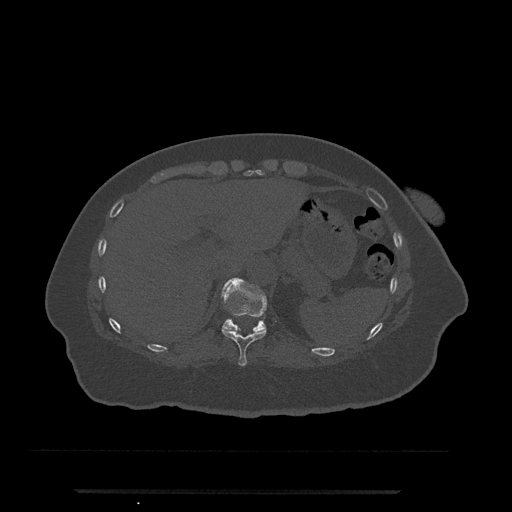
CT including the spine, one axial slice; position 262 of 797 along the scan axis; reconstruction kernel Br40s/3; 120 kVp; bone window (W 1800 / L 400 HU); 0.5 mm slice thickness; 512 × 512 image matrix. Female patient, age 51 years. From the clinical record (not read from this slice): primary cancer: neuro; vertebrae with lytic lesions (as recorded): T8.
Outlined on this slice (semi-automatic segmentation, software-assisted and operator-edited):
- T10 vertebra: bounding box <222,327,267,366> (left, top, right, bottom; pixels)
- T11 vertebra: <222,278,267,332>